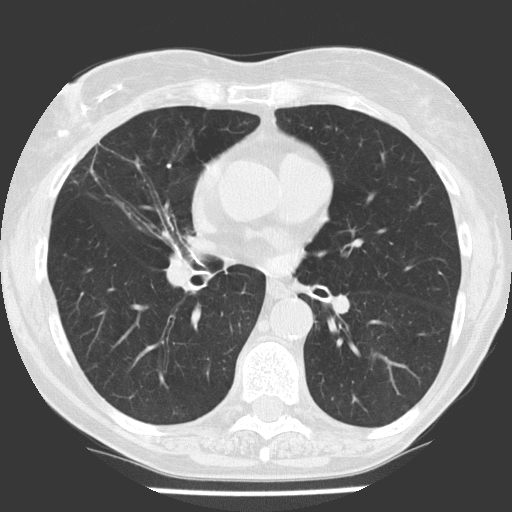
Axial slice from a low-dose chest CT screening exam; first (baseline) screen; lung window (W 1500 / L -600 HU); 2 mm slice thickness; 120 kVp; slice 73 of 147 in the series. Female, age 68 years at enrolment.
Expert reader's lesion annotation, bounding box [x1, y1, x2, y2] px = [337, 321, 398, 379]. No non-calcified nodule or mass ≥4 mm was recorded by the screening reader at this exam.